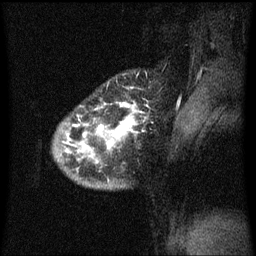
Breast MRI (dynamic contrast-enhanced), one sagittal slice. Slice 52 of 60 in the series (ordered by position). Dynamic contrast-enhanced series, image 2 of 3 at this slice position (ordered by acquisition). 1.5 T. TE 4.2 ms, TR 8.4 ms. 2 mm slice thickness. 256 × 256 image matrix. Female patient, age 34 years. Case-level facts recorded for this patient, not image findings: setting: breast cancer imaged before/during neoadjuvant chemotherapy; receptor status: HR-positive, HER2-negative.
Annotated regions visible in this slice (semi-automatic segmentation, software-assisted and operator-edited):
- analysis volume of interest (the breast-tissue region the enhancement analysis was run in; not a lesion): box from (x=54, y=78) to (x=155, y=191) px
- tumour enhancement mask (voxels above the 70 % enhancement threshold inside the analysis volume of interest): (x=66, y=102)–(x=143, y=153)